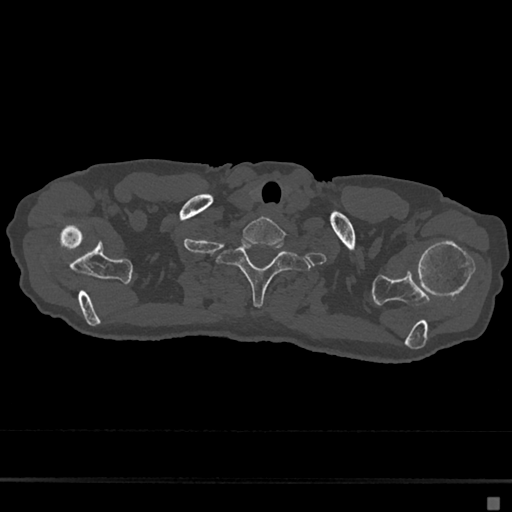
CT including the spine, one axial slice. Slice 614 of 797 in the series (ordered by position). Reconstruction kernel Br40s/3. Bone window (W 1800 / L 400 HU). 0.5 mm slice thickness. 512 × 512 image matrix, field of view 360 × 360 mm. Female patient, age 68 years. Case-level facts recorded for this patient, not image findings: primary cancer: renal.
Annotated regions visible in this slice (semi-automatic segmentation, software-assisted and operator-edited):
- T1 vertebra: bounding box <216,239,311,307> (left, top, right, bottom; pixels)